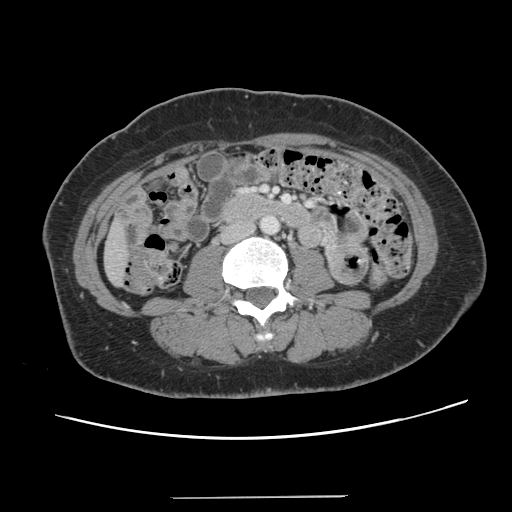
Contrast-enhanced abdominal CT, one axial slice; position 21 of 141 along the scan axis; 120 kVp; intravenous contrast given; soft-tissue window (W 400 / L 40 HU); 512 × 512 image matrix, field of view 366 × 366 mm. Female patient, age 53 years. Case-level facts recorded for this patient, not image findings: diagnosis: colorectal cancer liver metastases, imaged before liver resection; multiple liver metastases: no; largest metastasis: 14.5 cm; disease in both lobes: yes.
Structures marked on this image (manually delineated by an expert):
- liver: bounding box <106,223,129,284> (left, top, right, bottom; pixels)
- planned liver remnant (the part of the liver to remain after resection): <106,224,128,284>